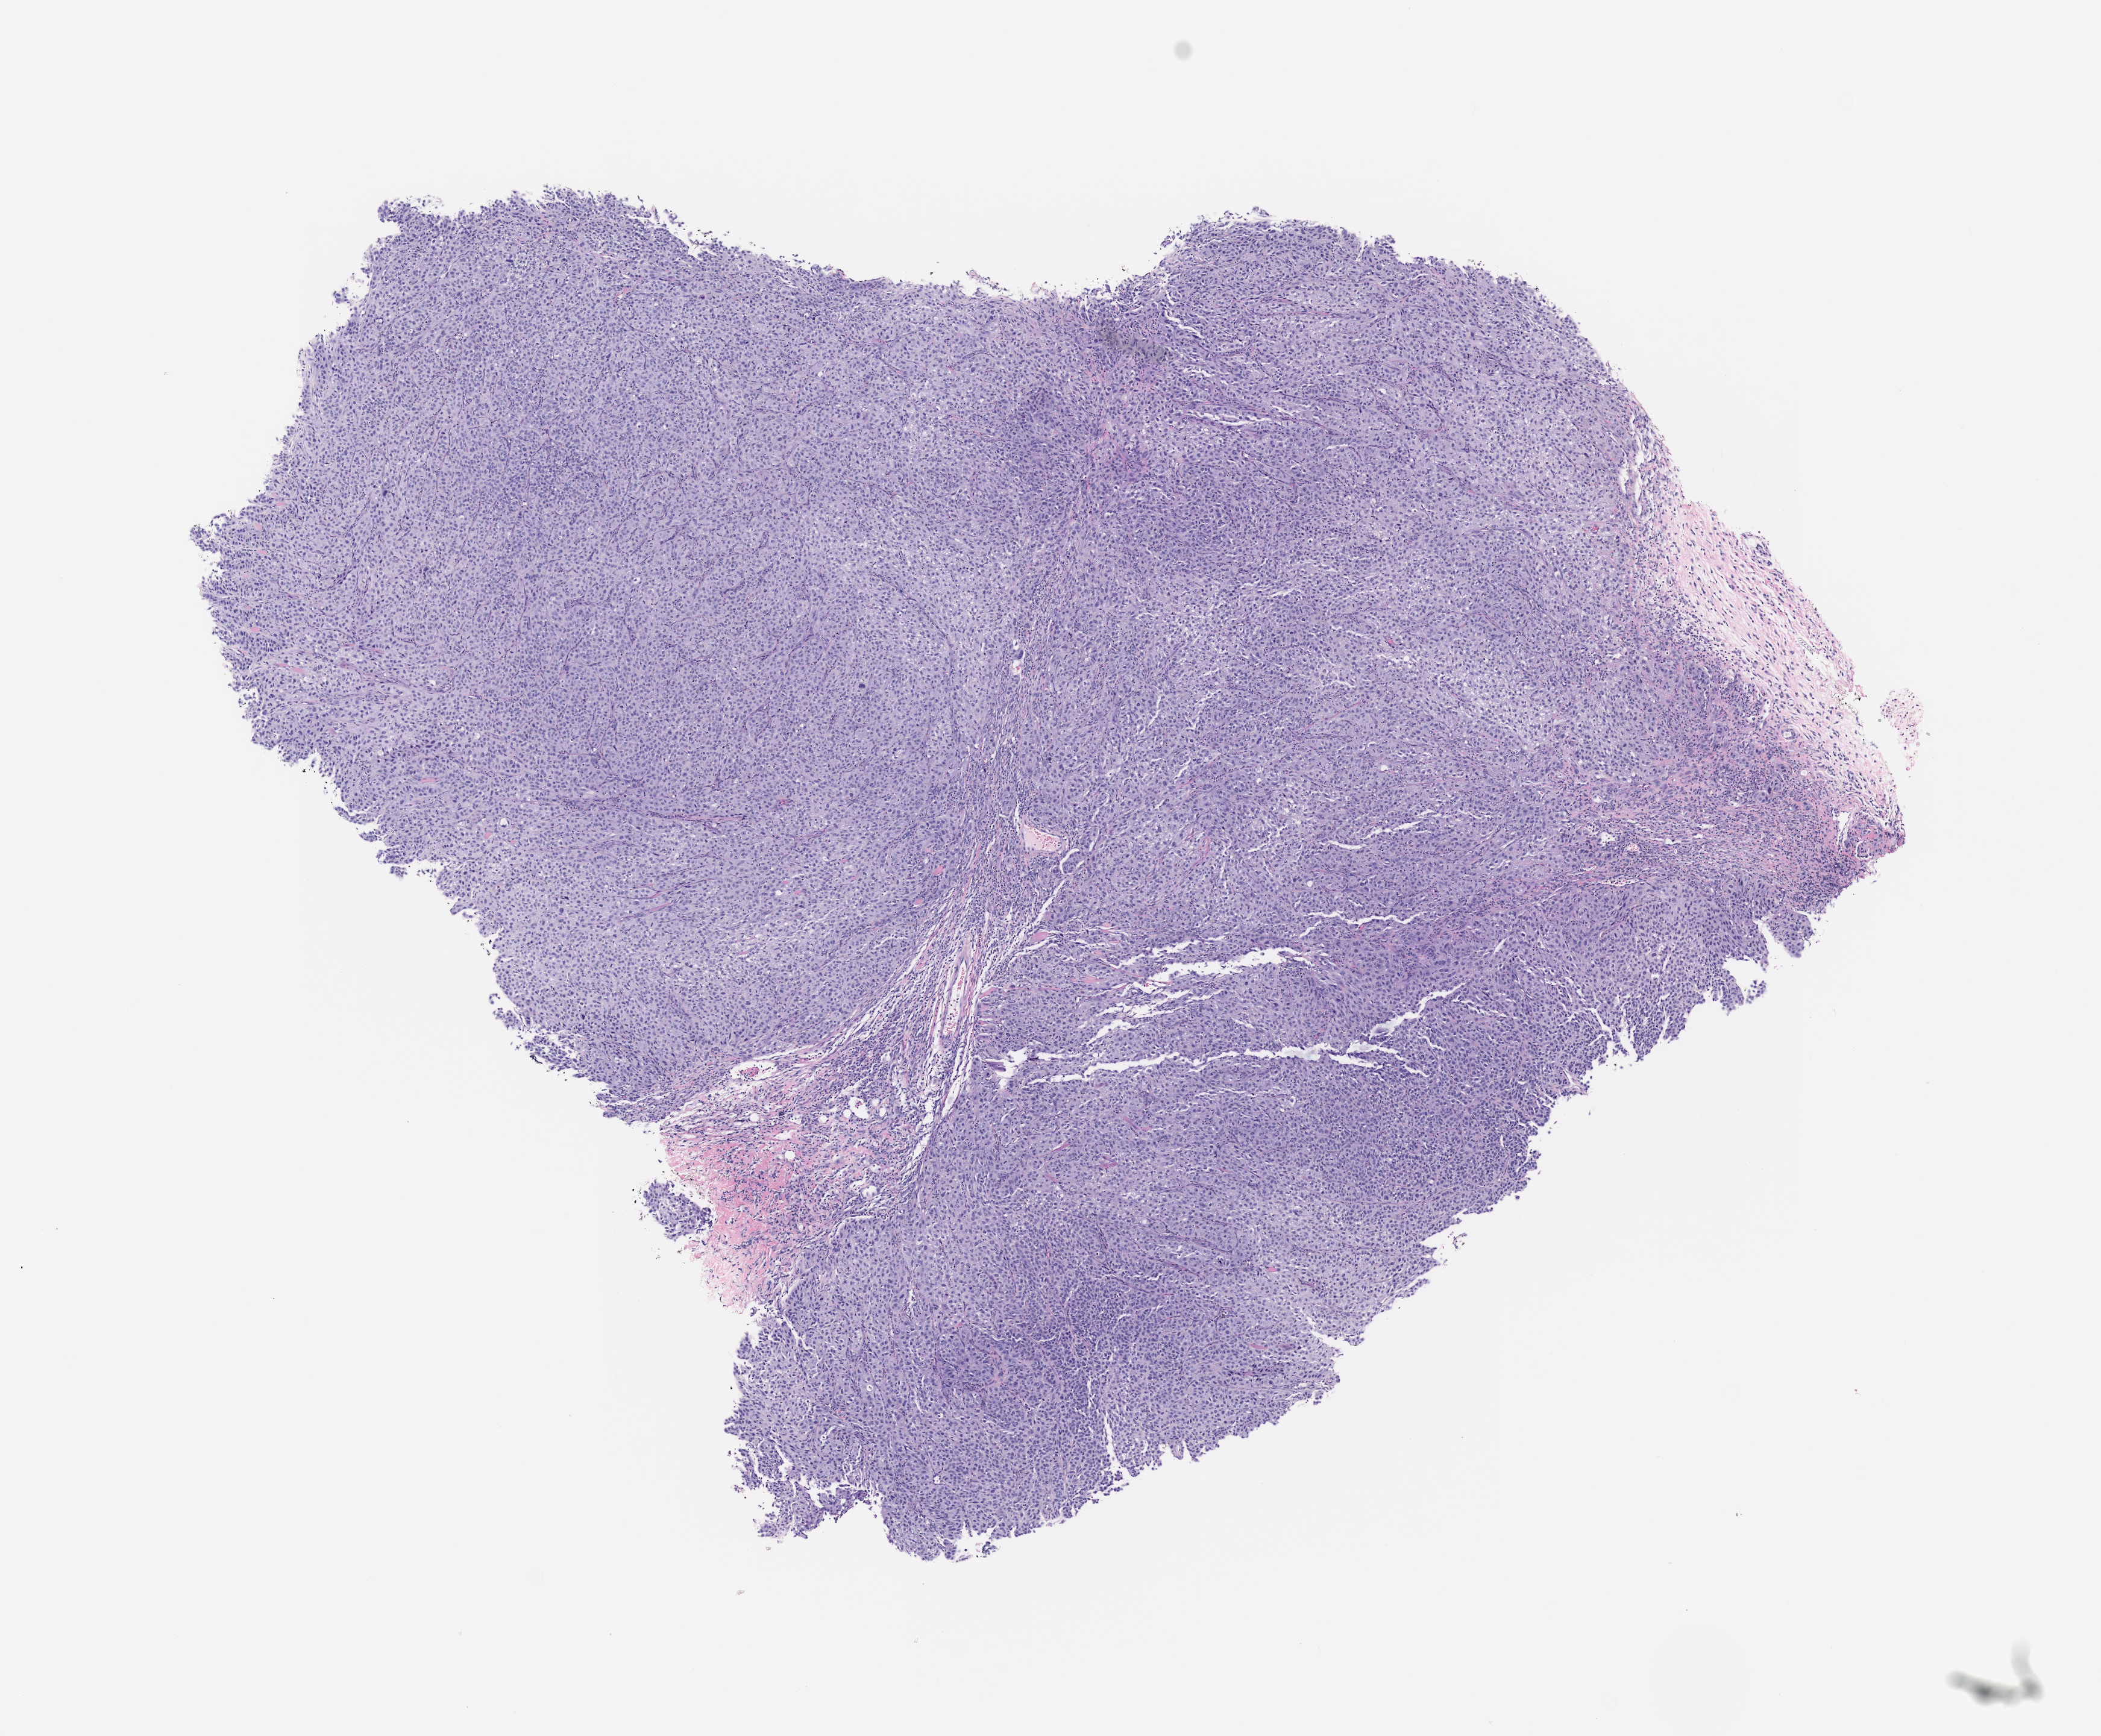
H&E whole-slide image of a patient-derived xenograft (PDX) tumor grown in a mouse, passage 5, a low-resolution overview of the entire scanned area, about 7.0 x 5.8 mm. Formalin-fixed paraffin-embedded section. Tumor site category: bladder.
Originating patient diagnosis: Transitional Cell Carcinoma.